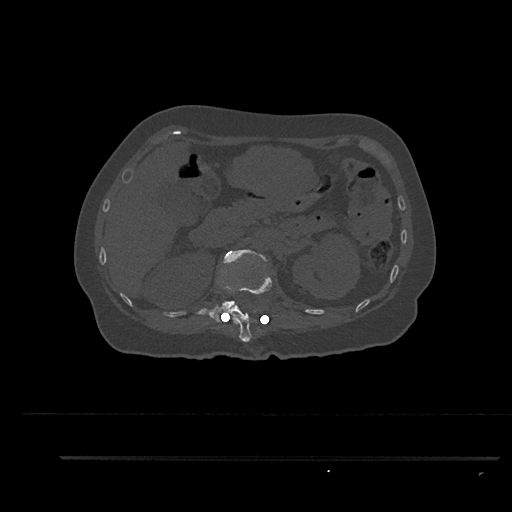
CT including the spine, one axial slice. 120 kVp. Bone window (W 1800 / L 400 HU). 0.5 mm slice thickness. 512 × 512 image matrix, field of view 408 × 408 mm. Female patient, age 44 years. From the clinical record (not read from this slice): primary cancer: renal; vertebrae with lytic lesions (as recorded): L1.
Outlined on this slice (semi-automatically segmented with operator editing):
- L1 vertebra: bounding box <209,249,269,318> (left, top, right, bottom; pixels)
- T12 vertebra: <212,256,272,344>